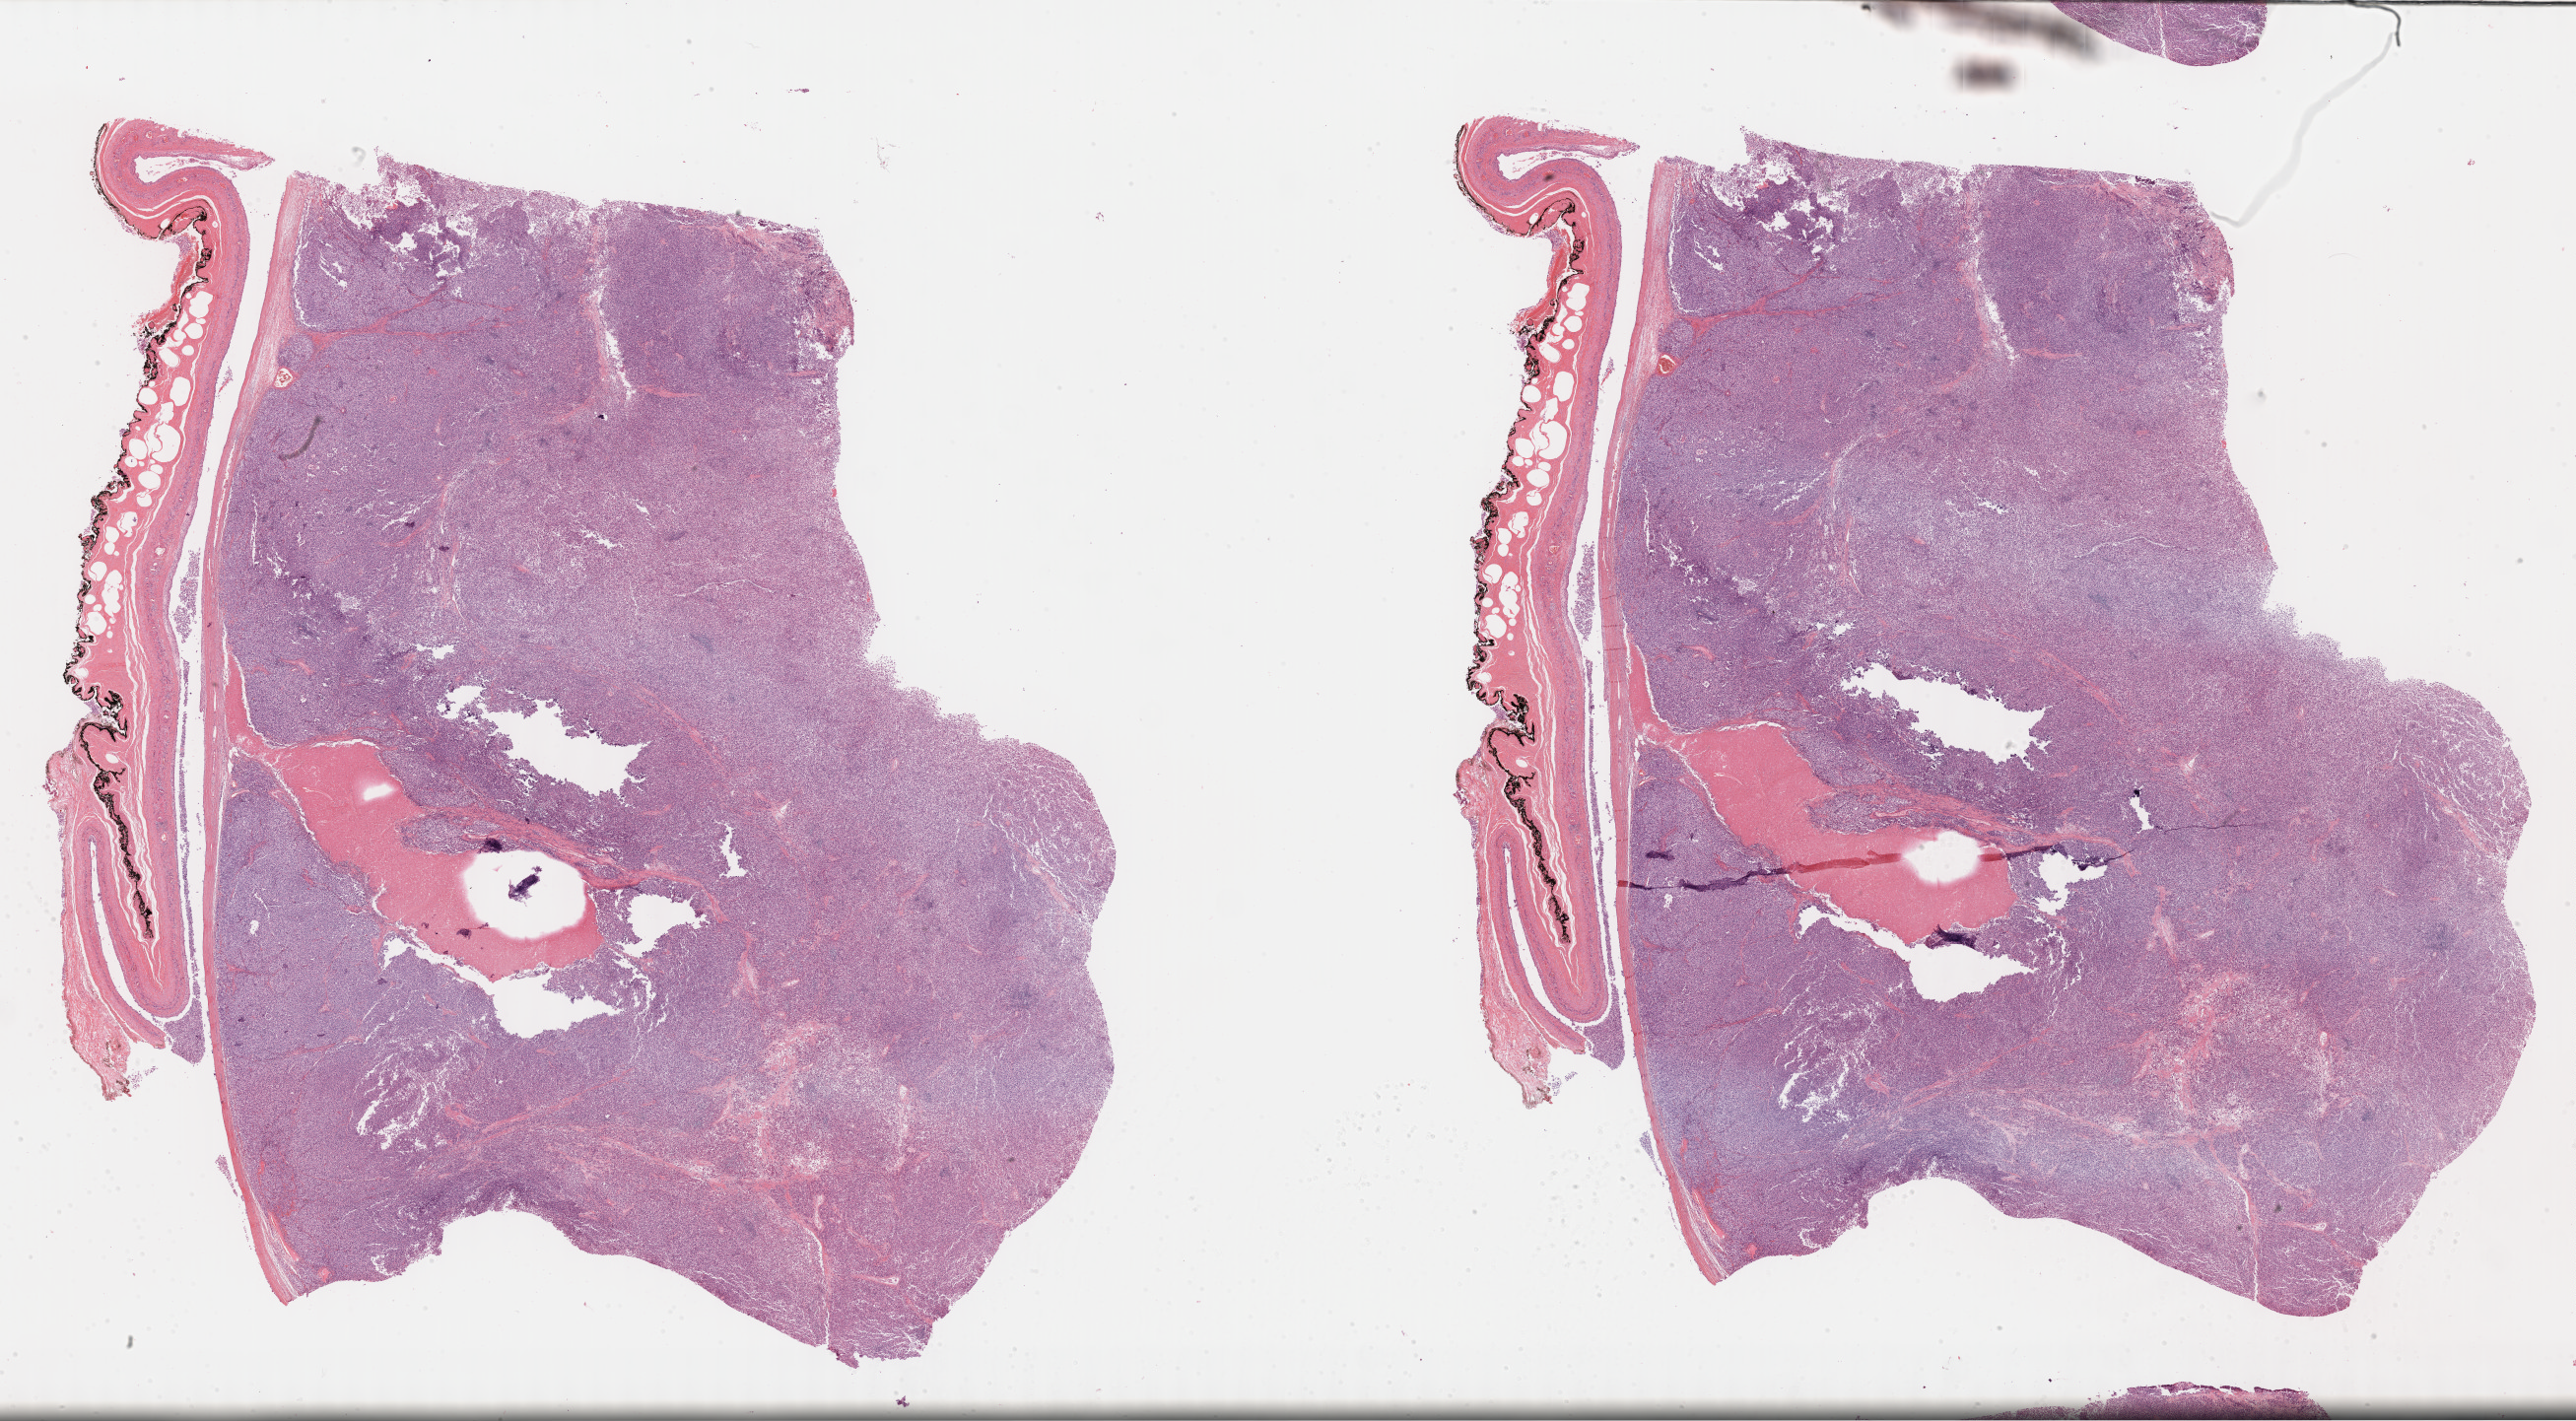
Digitized H&E-stained tissue section (whole slide), a low-resolution overview of the entire scanned area, about 42.3 x 23.3 mm (acquisition: 40x scan); formalin-fixed paraffin-embedded (FFPE) diagnostic section; sample: primary tumour, testis. Male, age 38 years at initial diagnosis.
- pathologic diagnosis: Seminoma, NOS
- AJCC pathologic stage: I (6th edition)
- laterality: left